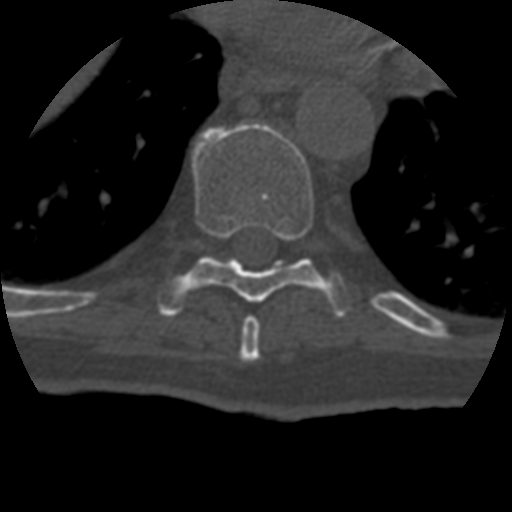
CT including the spine, one axial slice. Position 238 of 399 along the scan axis. Reconstruction kernel STANDARD. 120 kVp. Bone window (W 1800 / L 400 HU). 1.25 mm slice thickness. 512 × 512 image matrix. Patient age 69 years. Case-level facts recorded for this patient, not image findings: primary cancer: prostate.
Structures marked on this image (semi-automatically segmented with operator editing):
- T8 vertebra: bounding box [x1, y1, x2, y2] px = [239, 316, 260, 362]
- T9 vertebra: [159, 122, 347, 317]